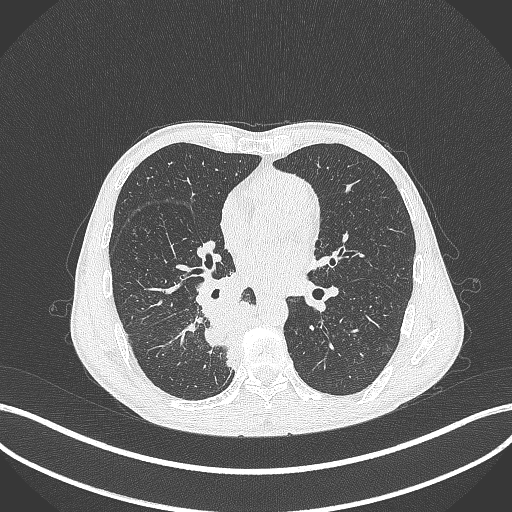
Chest CT, one axial slice; position 183 of 371 along the scan axis; 120 kVp; lung window (W 1500 / L -600 HU); 512 × 512 image matrix, field of view 400 × 400 mm. Male patient, age 58 years. From the clinical record (not read from this slice): clinical TNM (as recorded): T3 N1 M1.
Annotated regions visible in this slice (bounding box drawn by a radiologist):
- lung tumour (recorded histology: squamous cell carcinoma): bounding box [x1, y1, x2, y2] px = [205, 299, 271, 373]